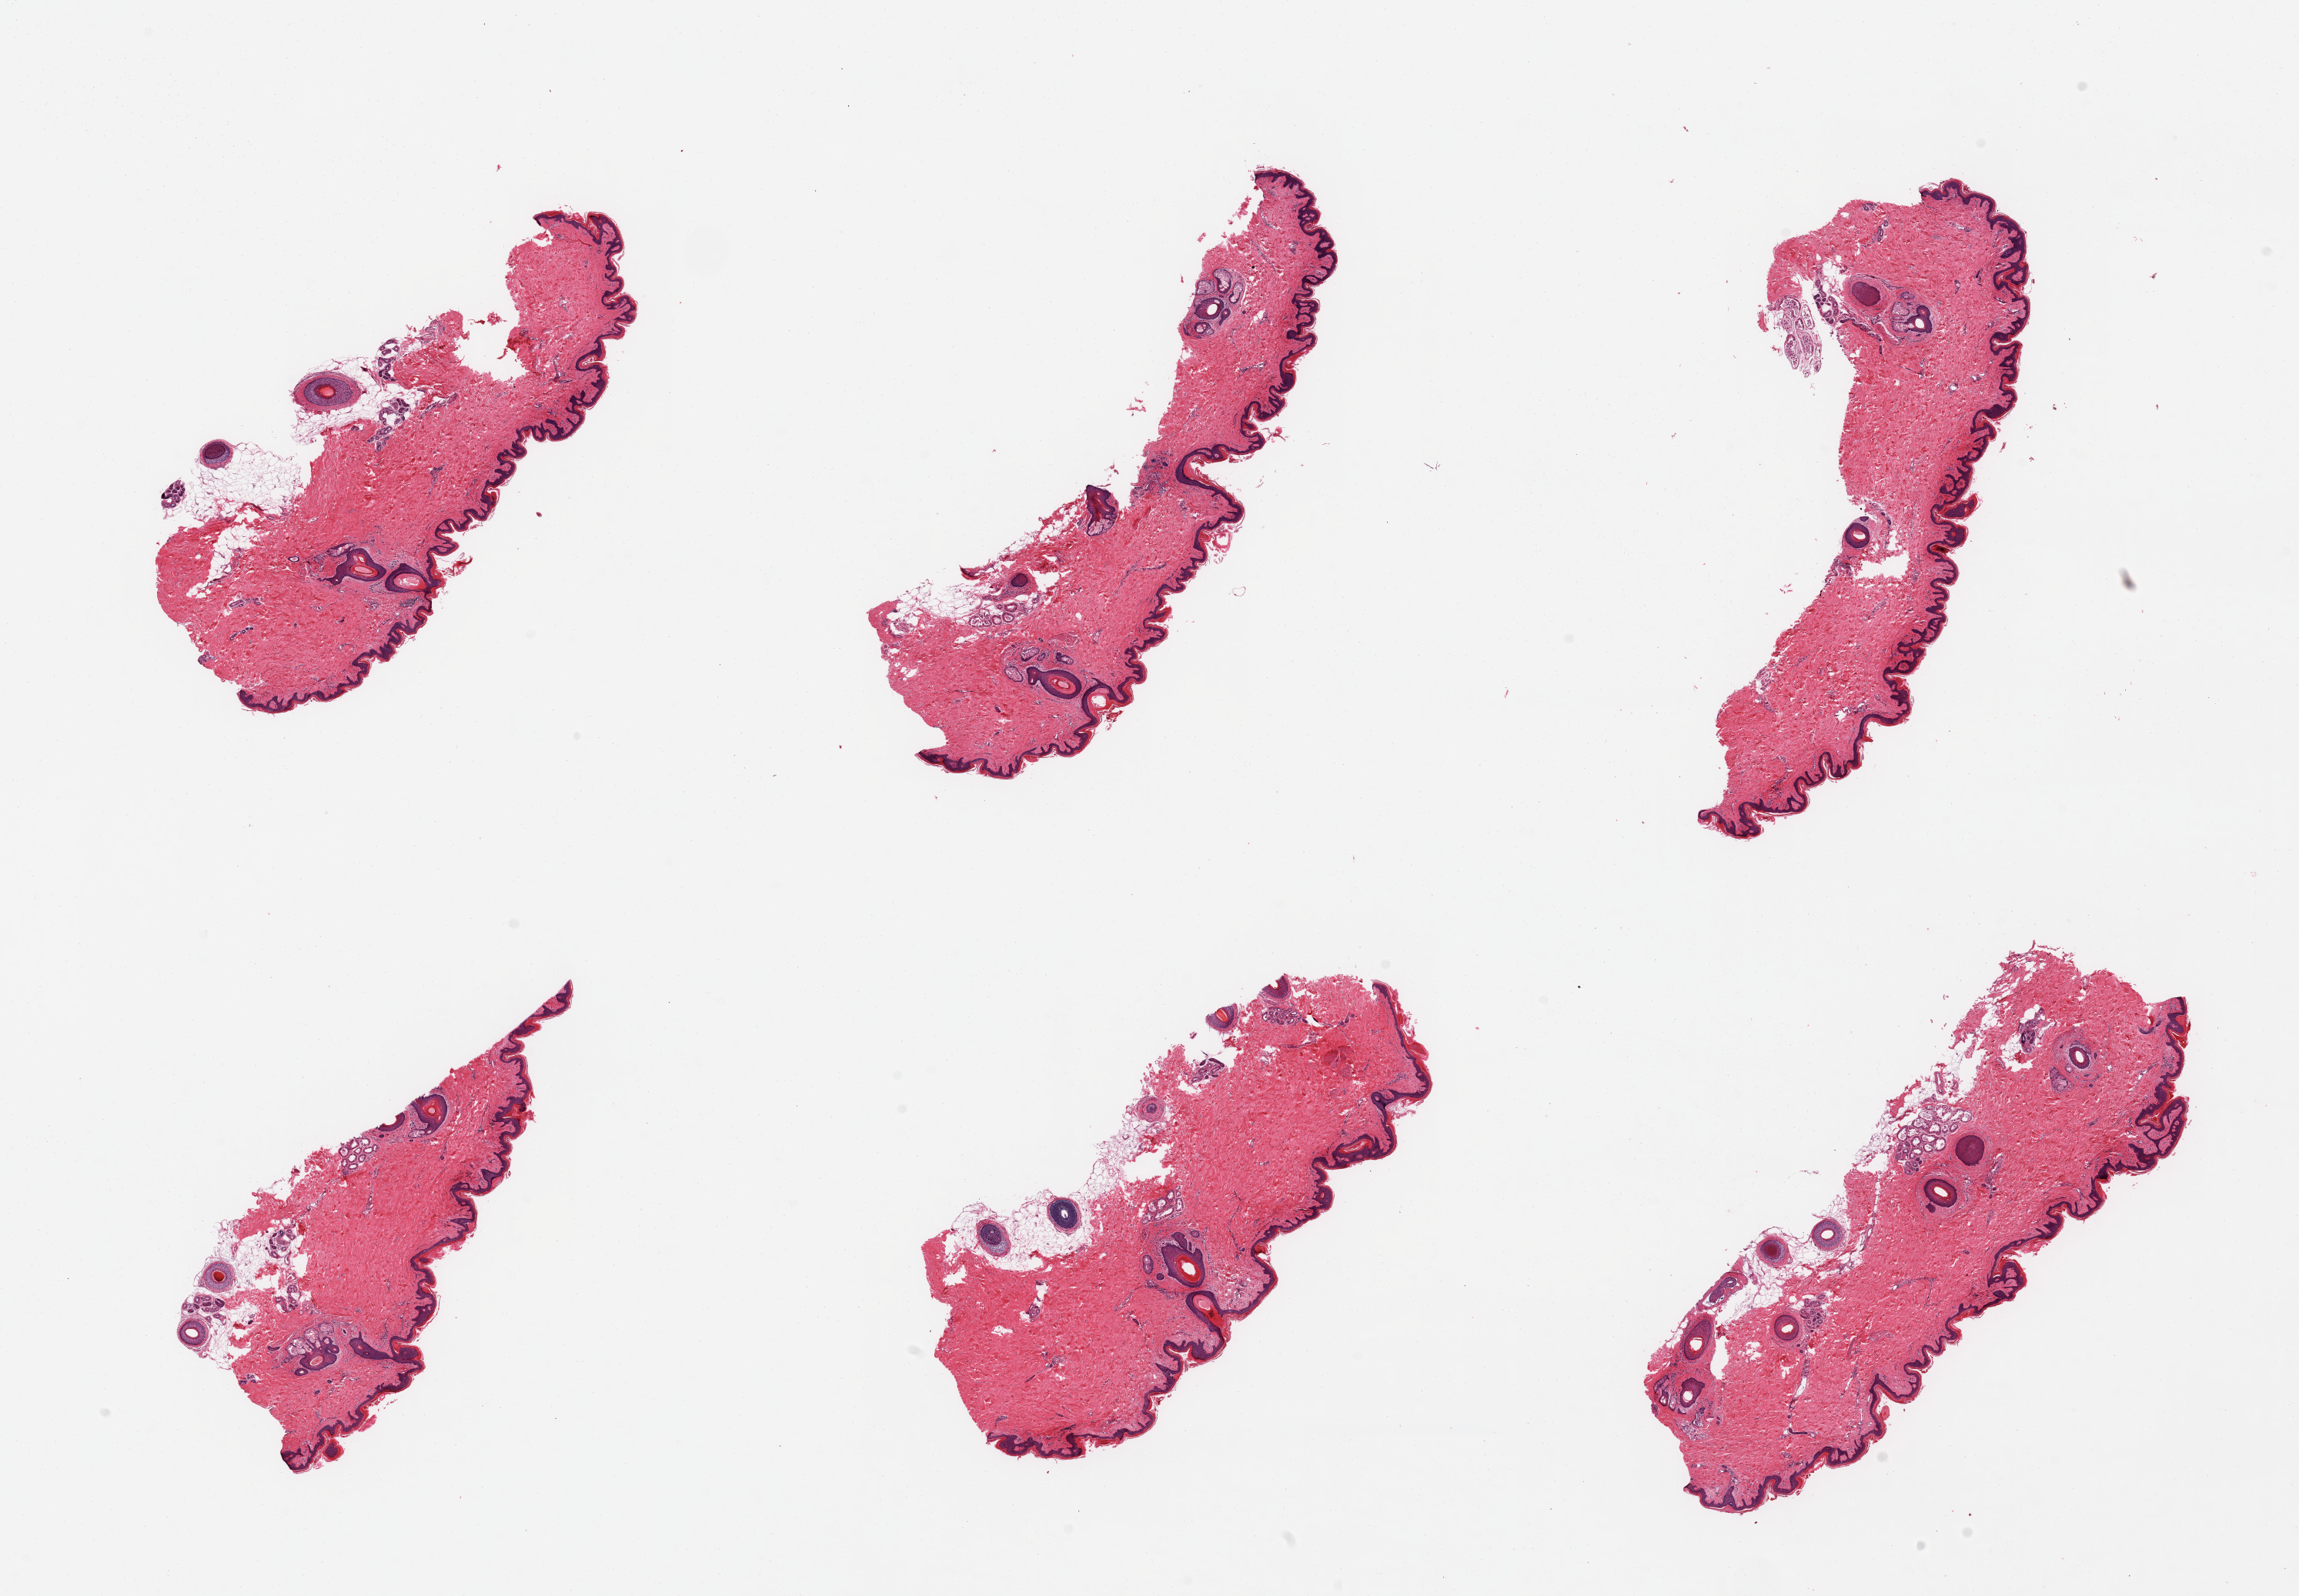
Digitized haematoxylin and eosin-stained section — whole scanned area (about 23.6 x 16.4 mm, slide scanned at 20x) shown as a low-resolution overview; PAXgene-fixed paraffin-embedded (PFPE) section; target tissue: skin of suprapubic region; donor tissue sample.
Pathologist's review note for this sample: 6 pieces, trace dermal fat; squamous epithelium is ~30-40 microns.